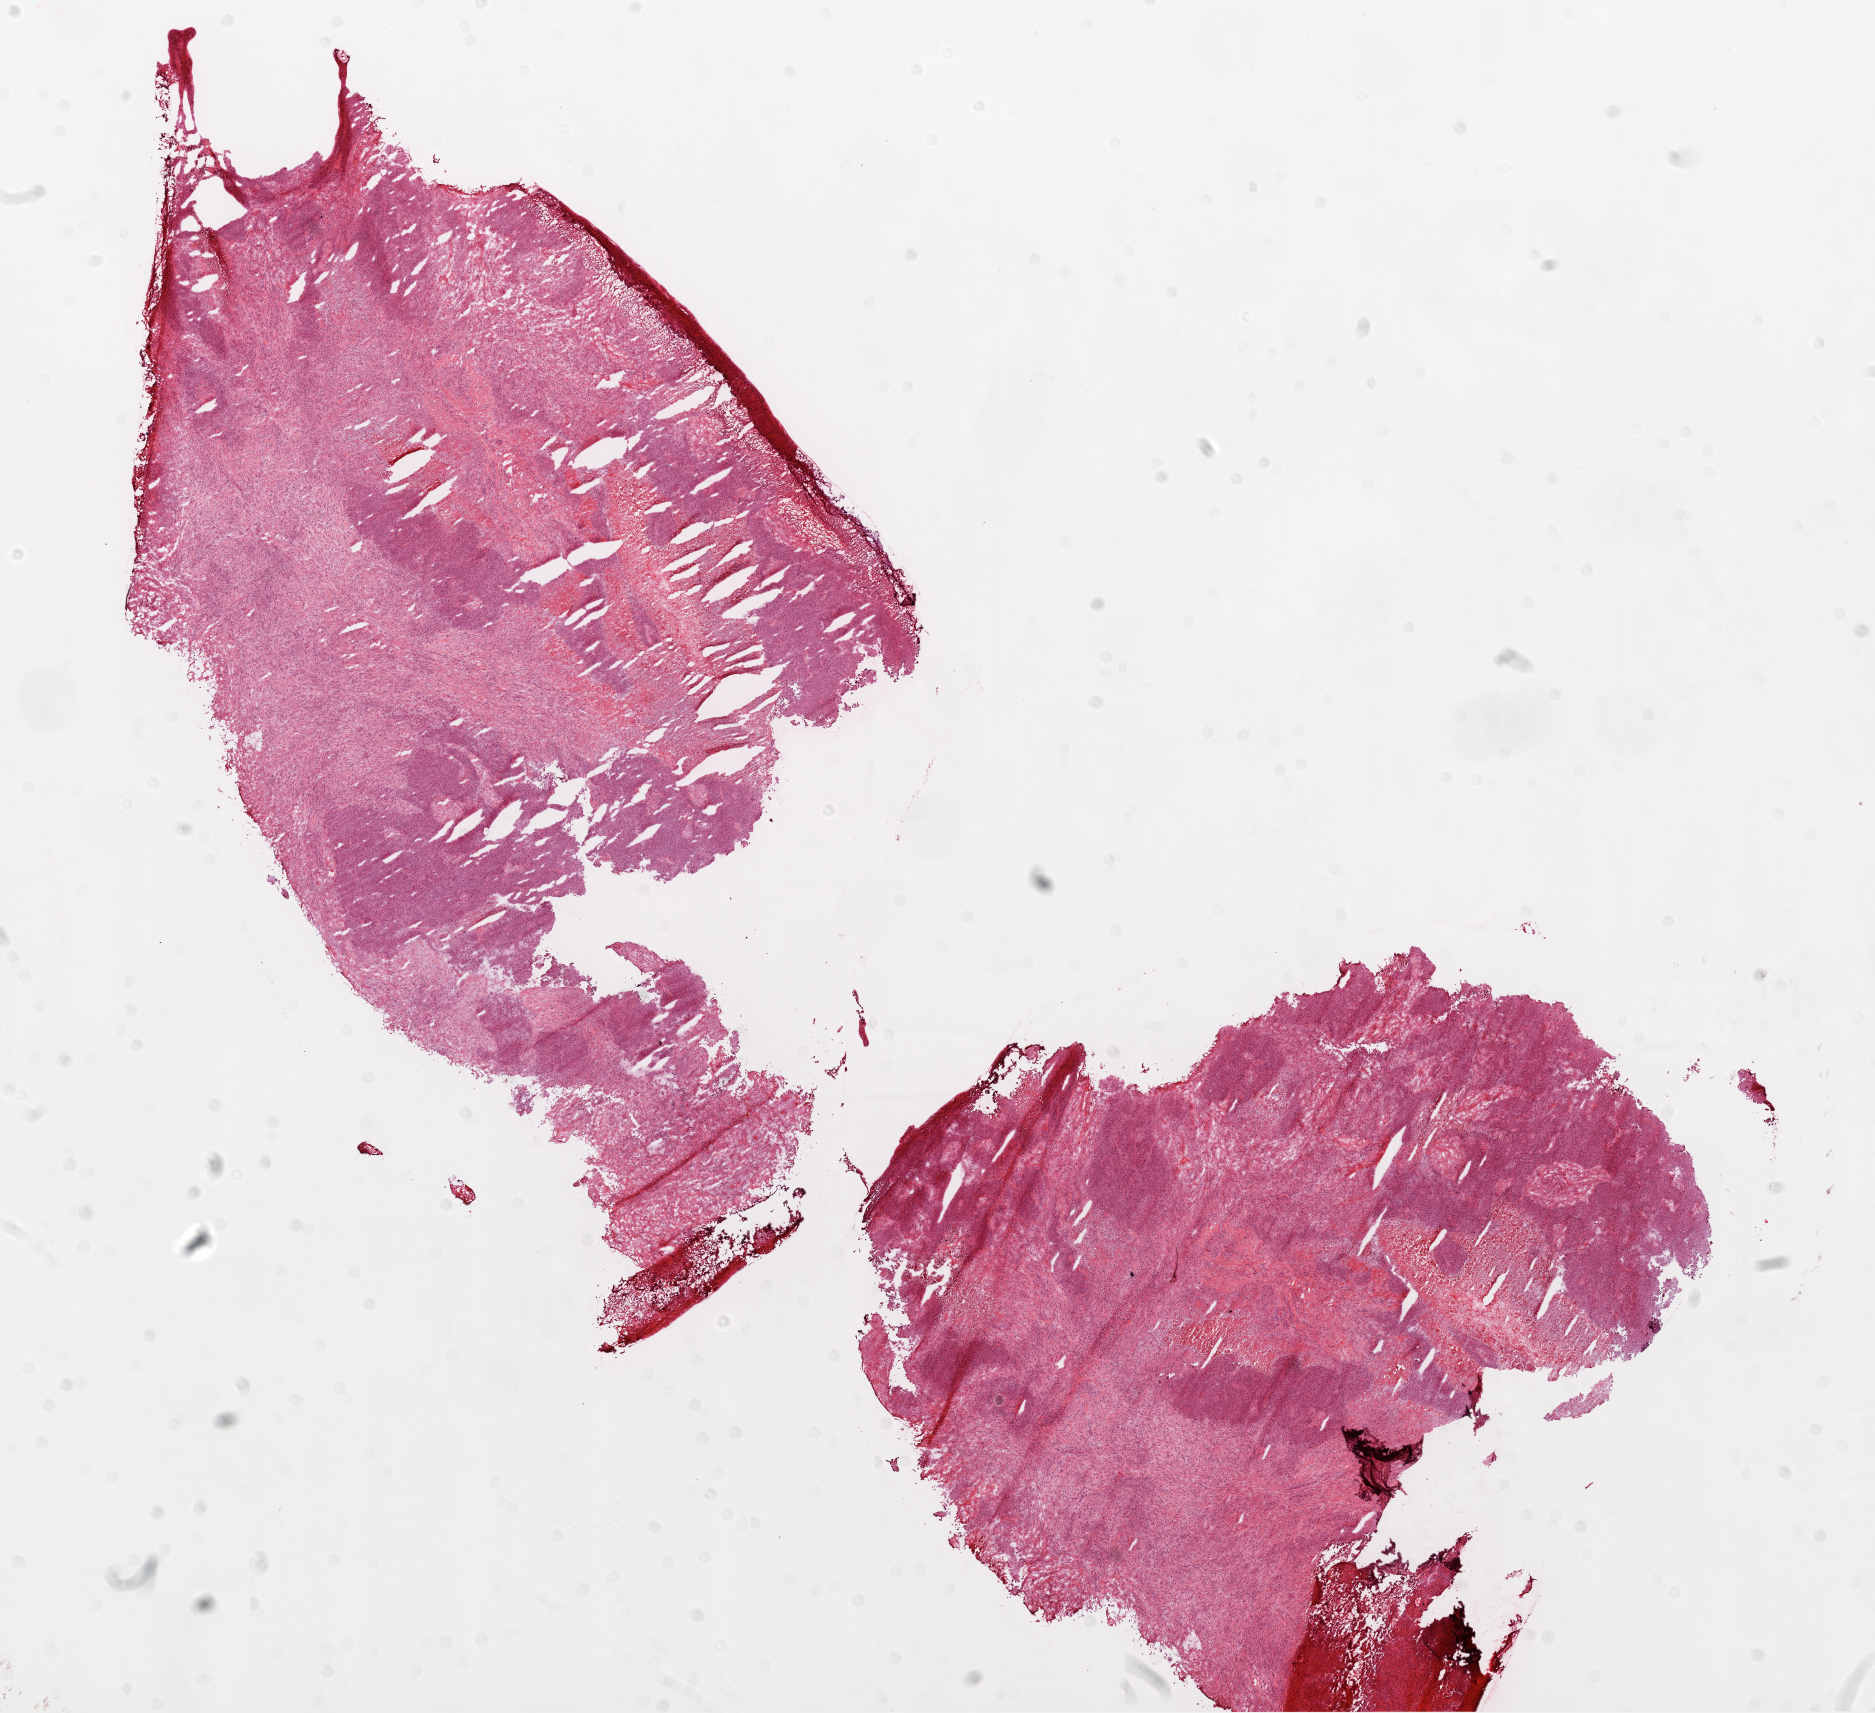
Hematoxylin and eosin (H&E) stained whole-slide image, a low-resolution overview of the entire scanned area, about 15.0 x 13.7 mm (slide scanned at 20x), frozen section from the top of the tissue portion, primary tumour sample from the ovary. Patient: female, age at initial diagnosis 60 years.
Diagnosis: Serous cystadenocarcinoma, NOS.